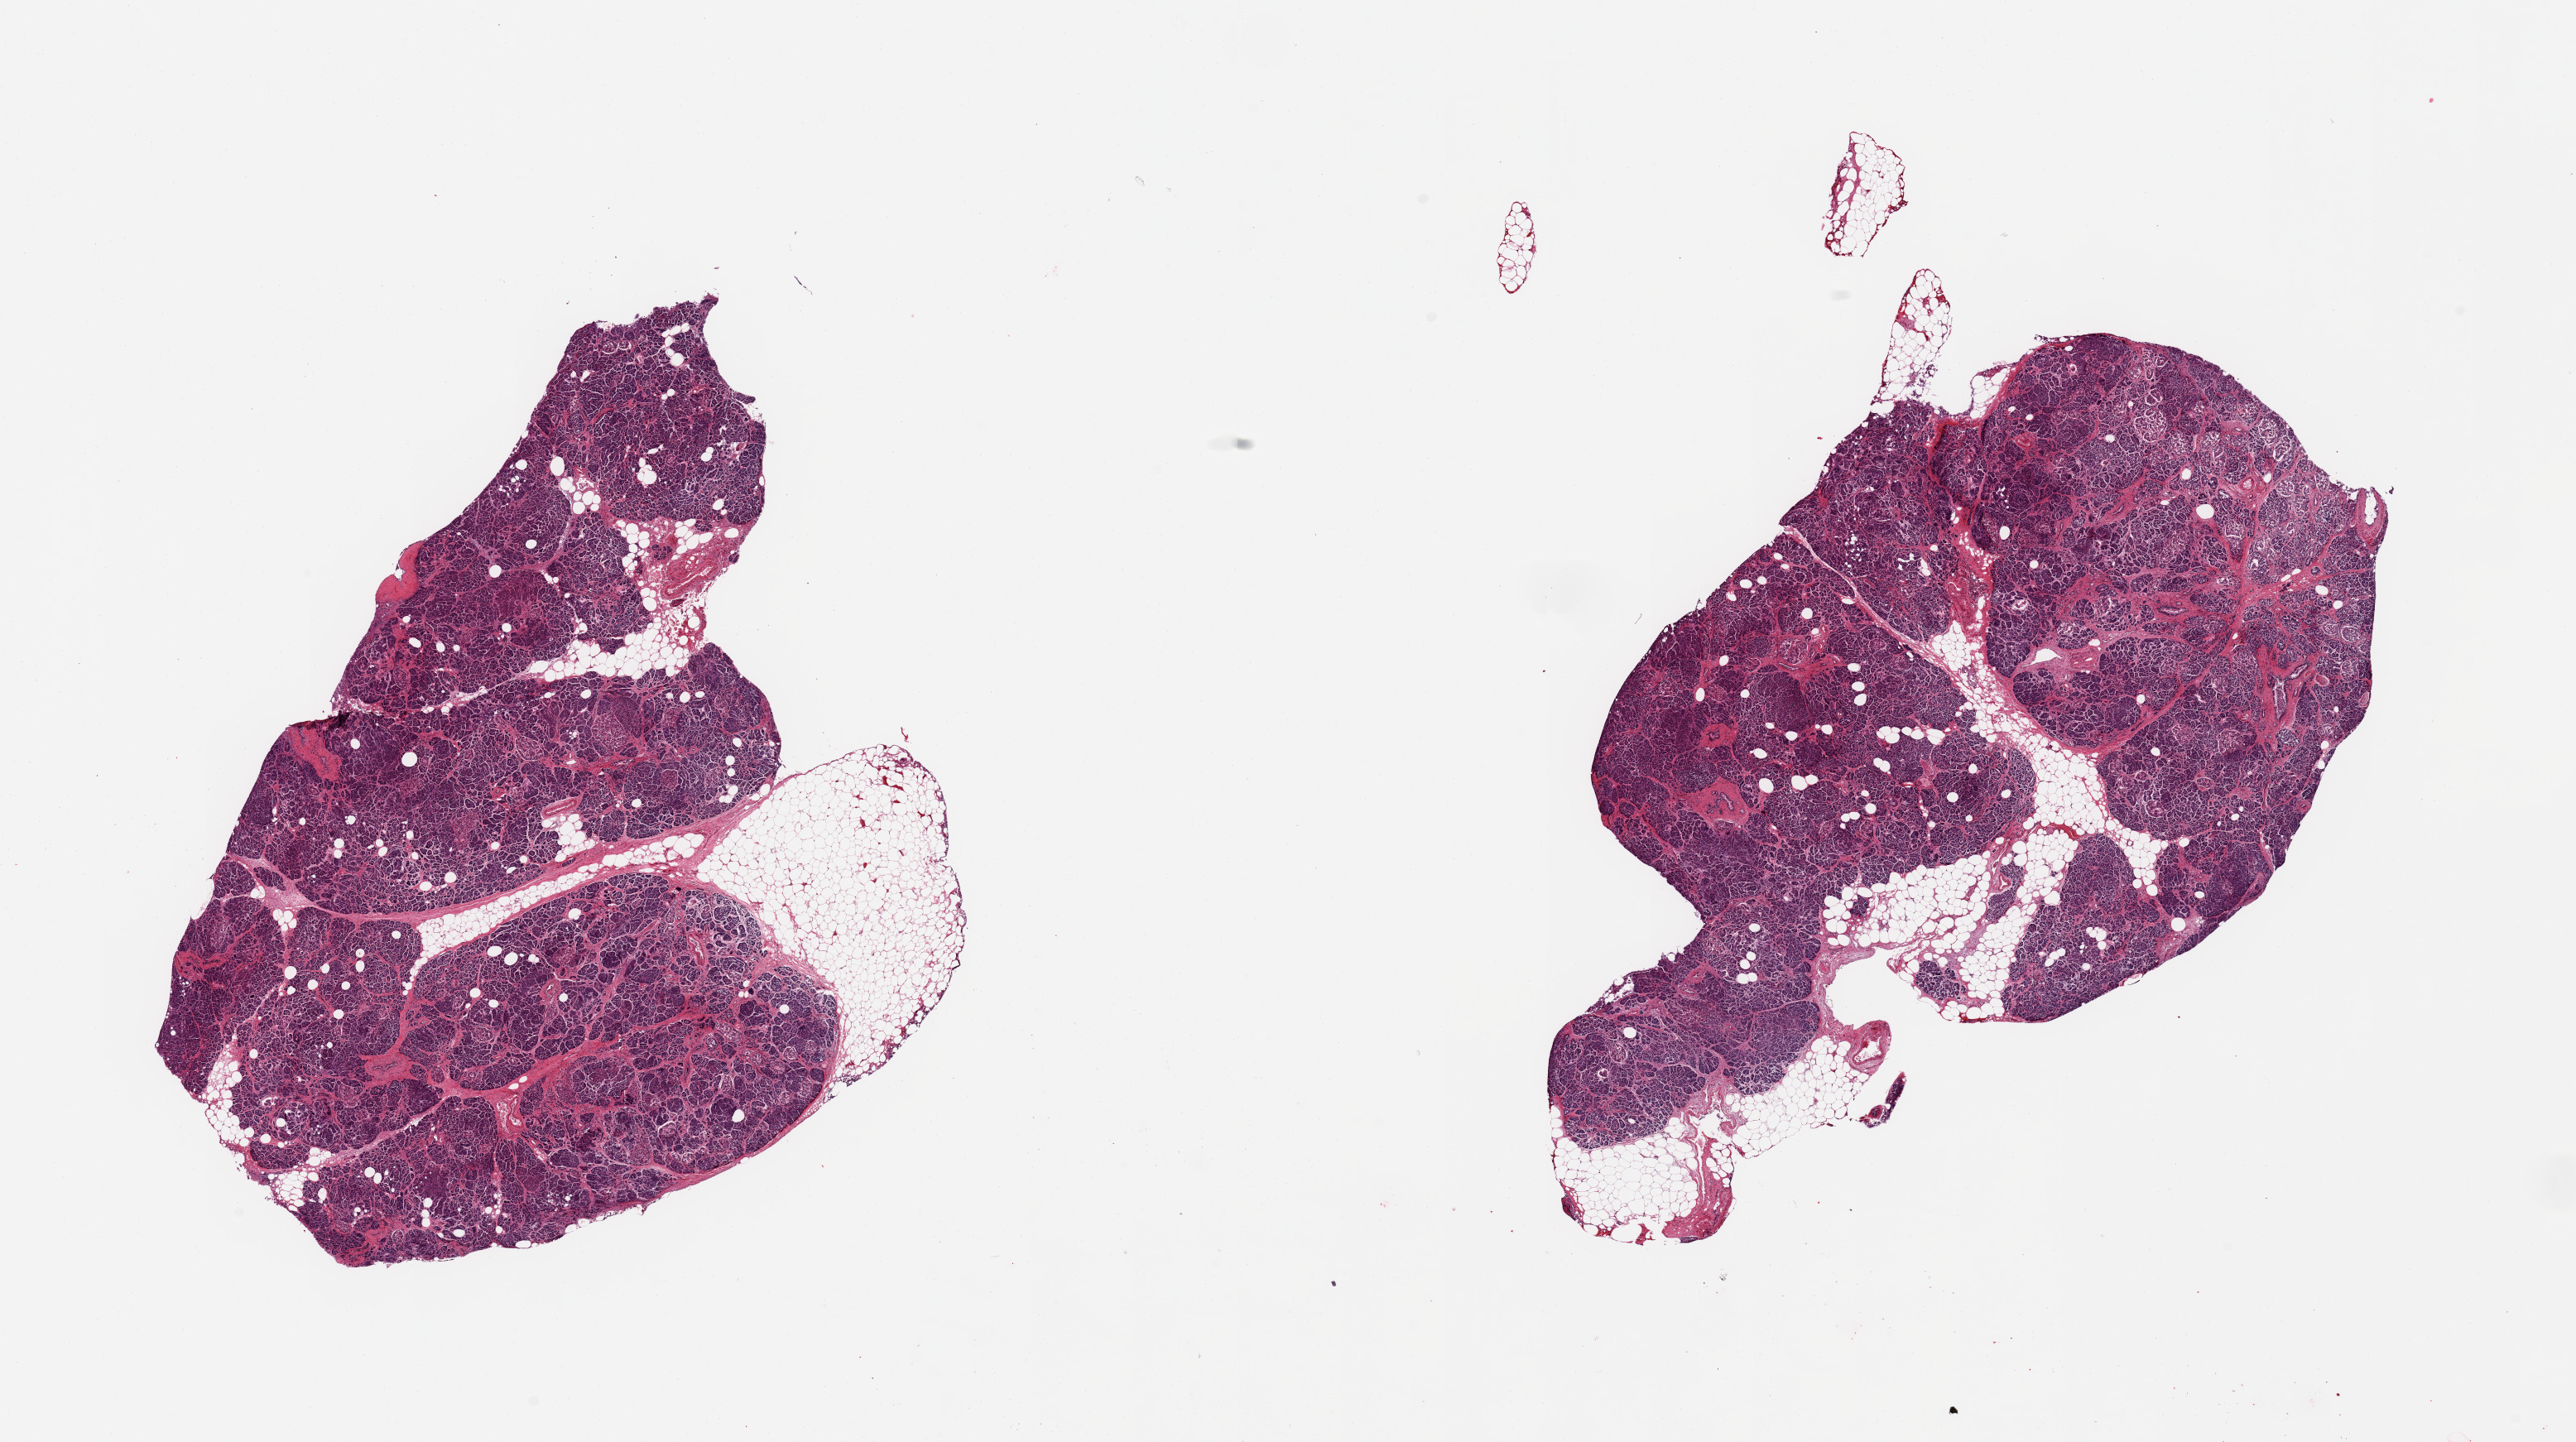
Digitized H&E-stained section, shown as a low-resolution overview of the whole scanned area (about 24.6 x 13.8 mm, acquisition: 20x scan). PAXgene-fixed paraffin-embedded (PFPE) section. Sampled site (target tissue): pancreas. Donor tissue sample. Donor: male.
Review note (as recorded): 2 pieces; includes 10-15% mostly attached fat, inter/intralobular fibrosis.